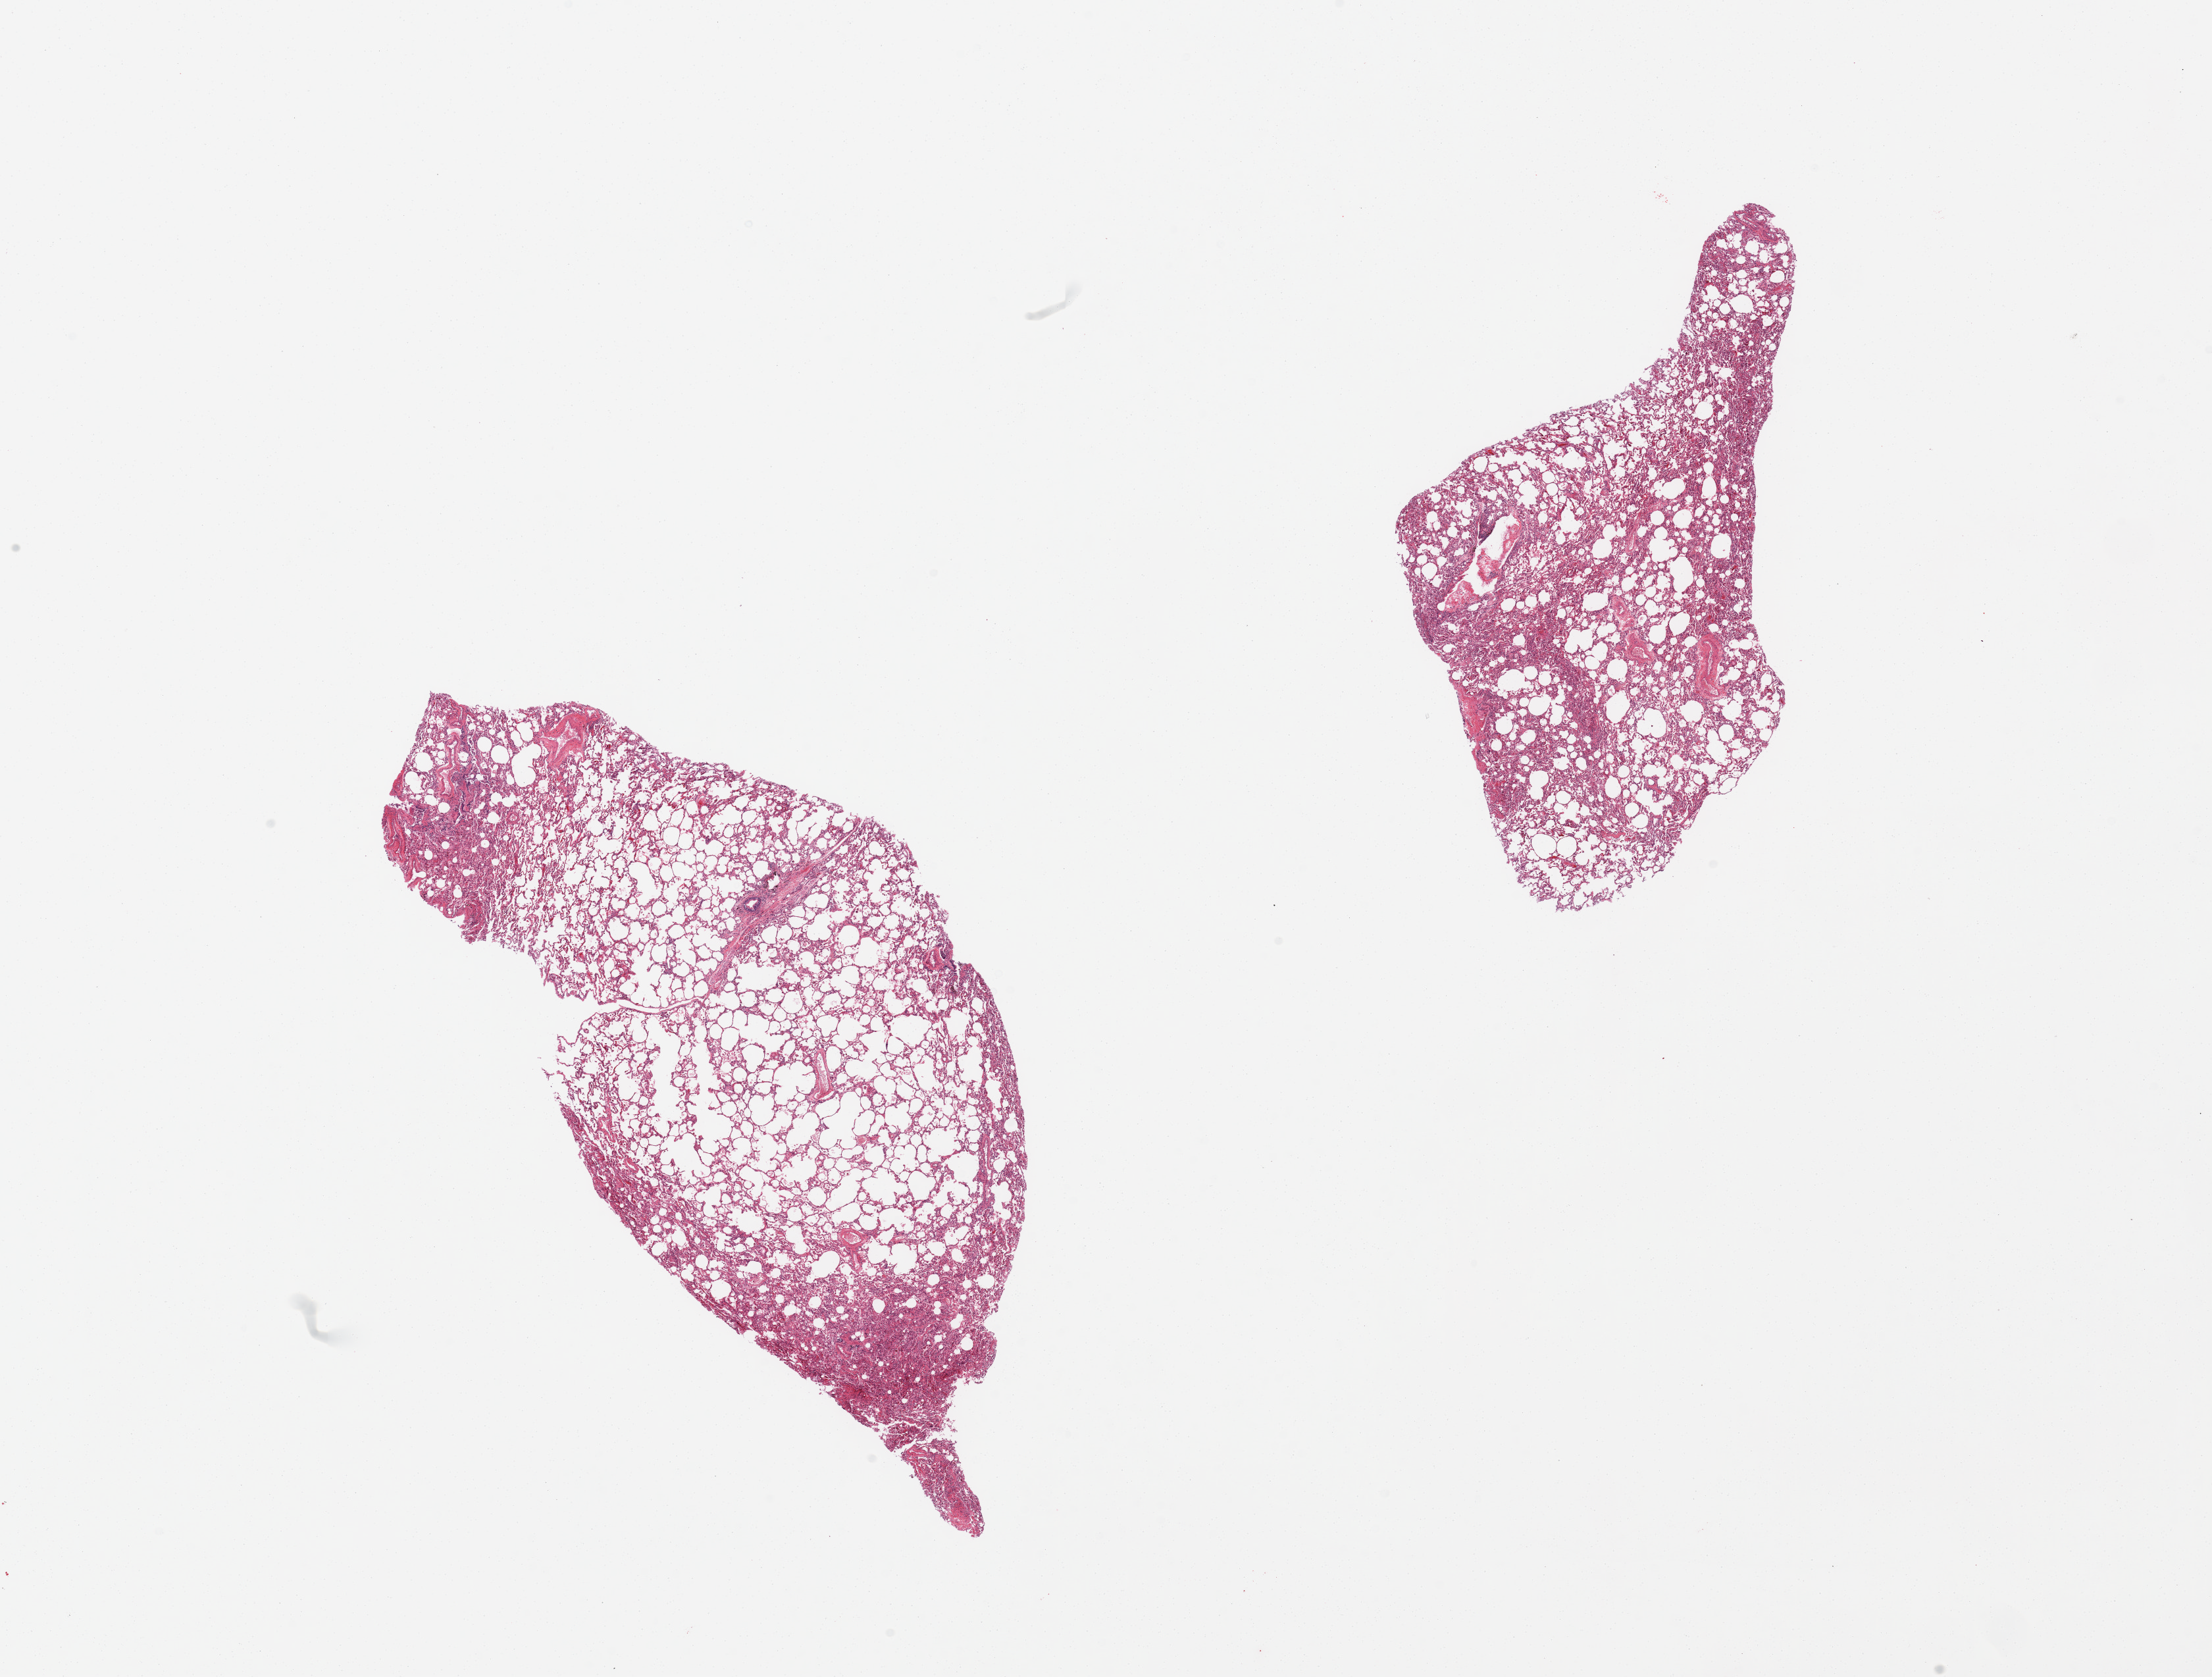
Haematoxylin and eosin whole-slide image, a low-resolution overview of the entire scanned area, about 26.6 x 20.2 mm; PAXgene-fixed, paraffin-embedded tissue; sampled site (target tissue): lung; tissue donor sample.
- pathologist's review note for this sample: 2 pieces, patchy congrestion, fibrin deposition